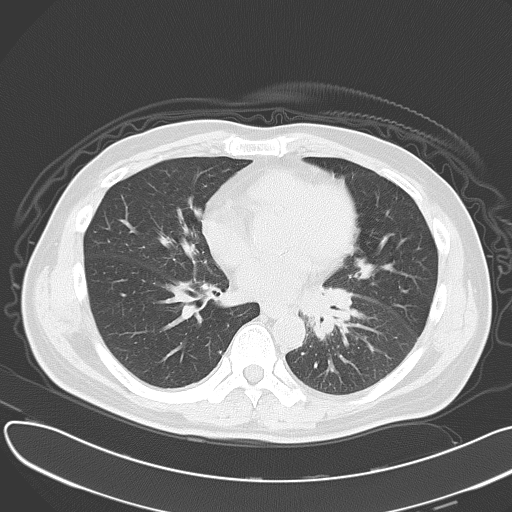
Chest CT, one axial slice; slice 24 of 55 in the series (ordered by position); reconstruction kernel B70f; lung window (W 1500 / L -600 HU); 5 mm slice thickness; 512 × 512 image matrix, field of view 376 × 376 mm. Male patient, age 55 years. From the clinical record (not read from this slice): clinical TNM (as recorded): T2 N3 M0.
Outlined on this slice (bounding box drawn by a radiologist):
- lung tumour (recorded histology: small cell carcinoma): box from (x=303, y=284) to (x=361, y=350) px